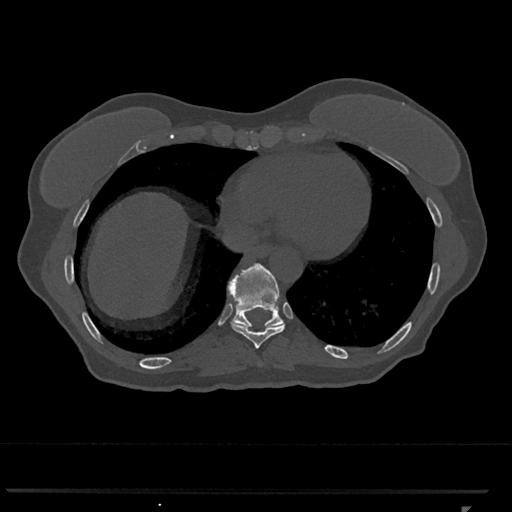
CT including the spine, one axial slice. Slice 601 of 793 in the series (ordered by position). Reconstruction kernel Br40s/3. 120 kVp. Bone window (W 1800 / L 400 HU). 0.5 mm slice thickness. 512 × 512 image matrix, field of view 380 × 380 mm. Patient: female, 62 years. From the clinical record (not read from this slice): primary cancer: renal.
Structures marked on this image (semi-automatic segmentation, software-assisted and operator-edited):
- T10 vertebra: bounding box (x1, y1, x2, y2) in pixels: (228, 263, 283, 328)
- T9 vertebra: (230, 306, 285, 349)